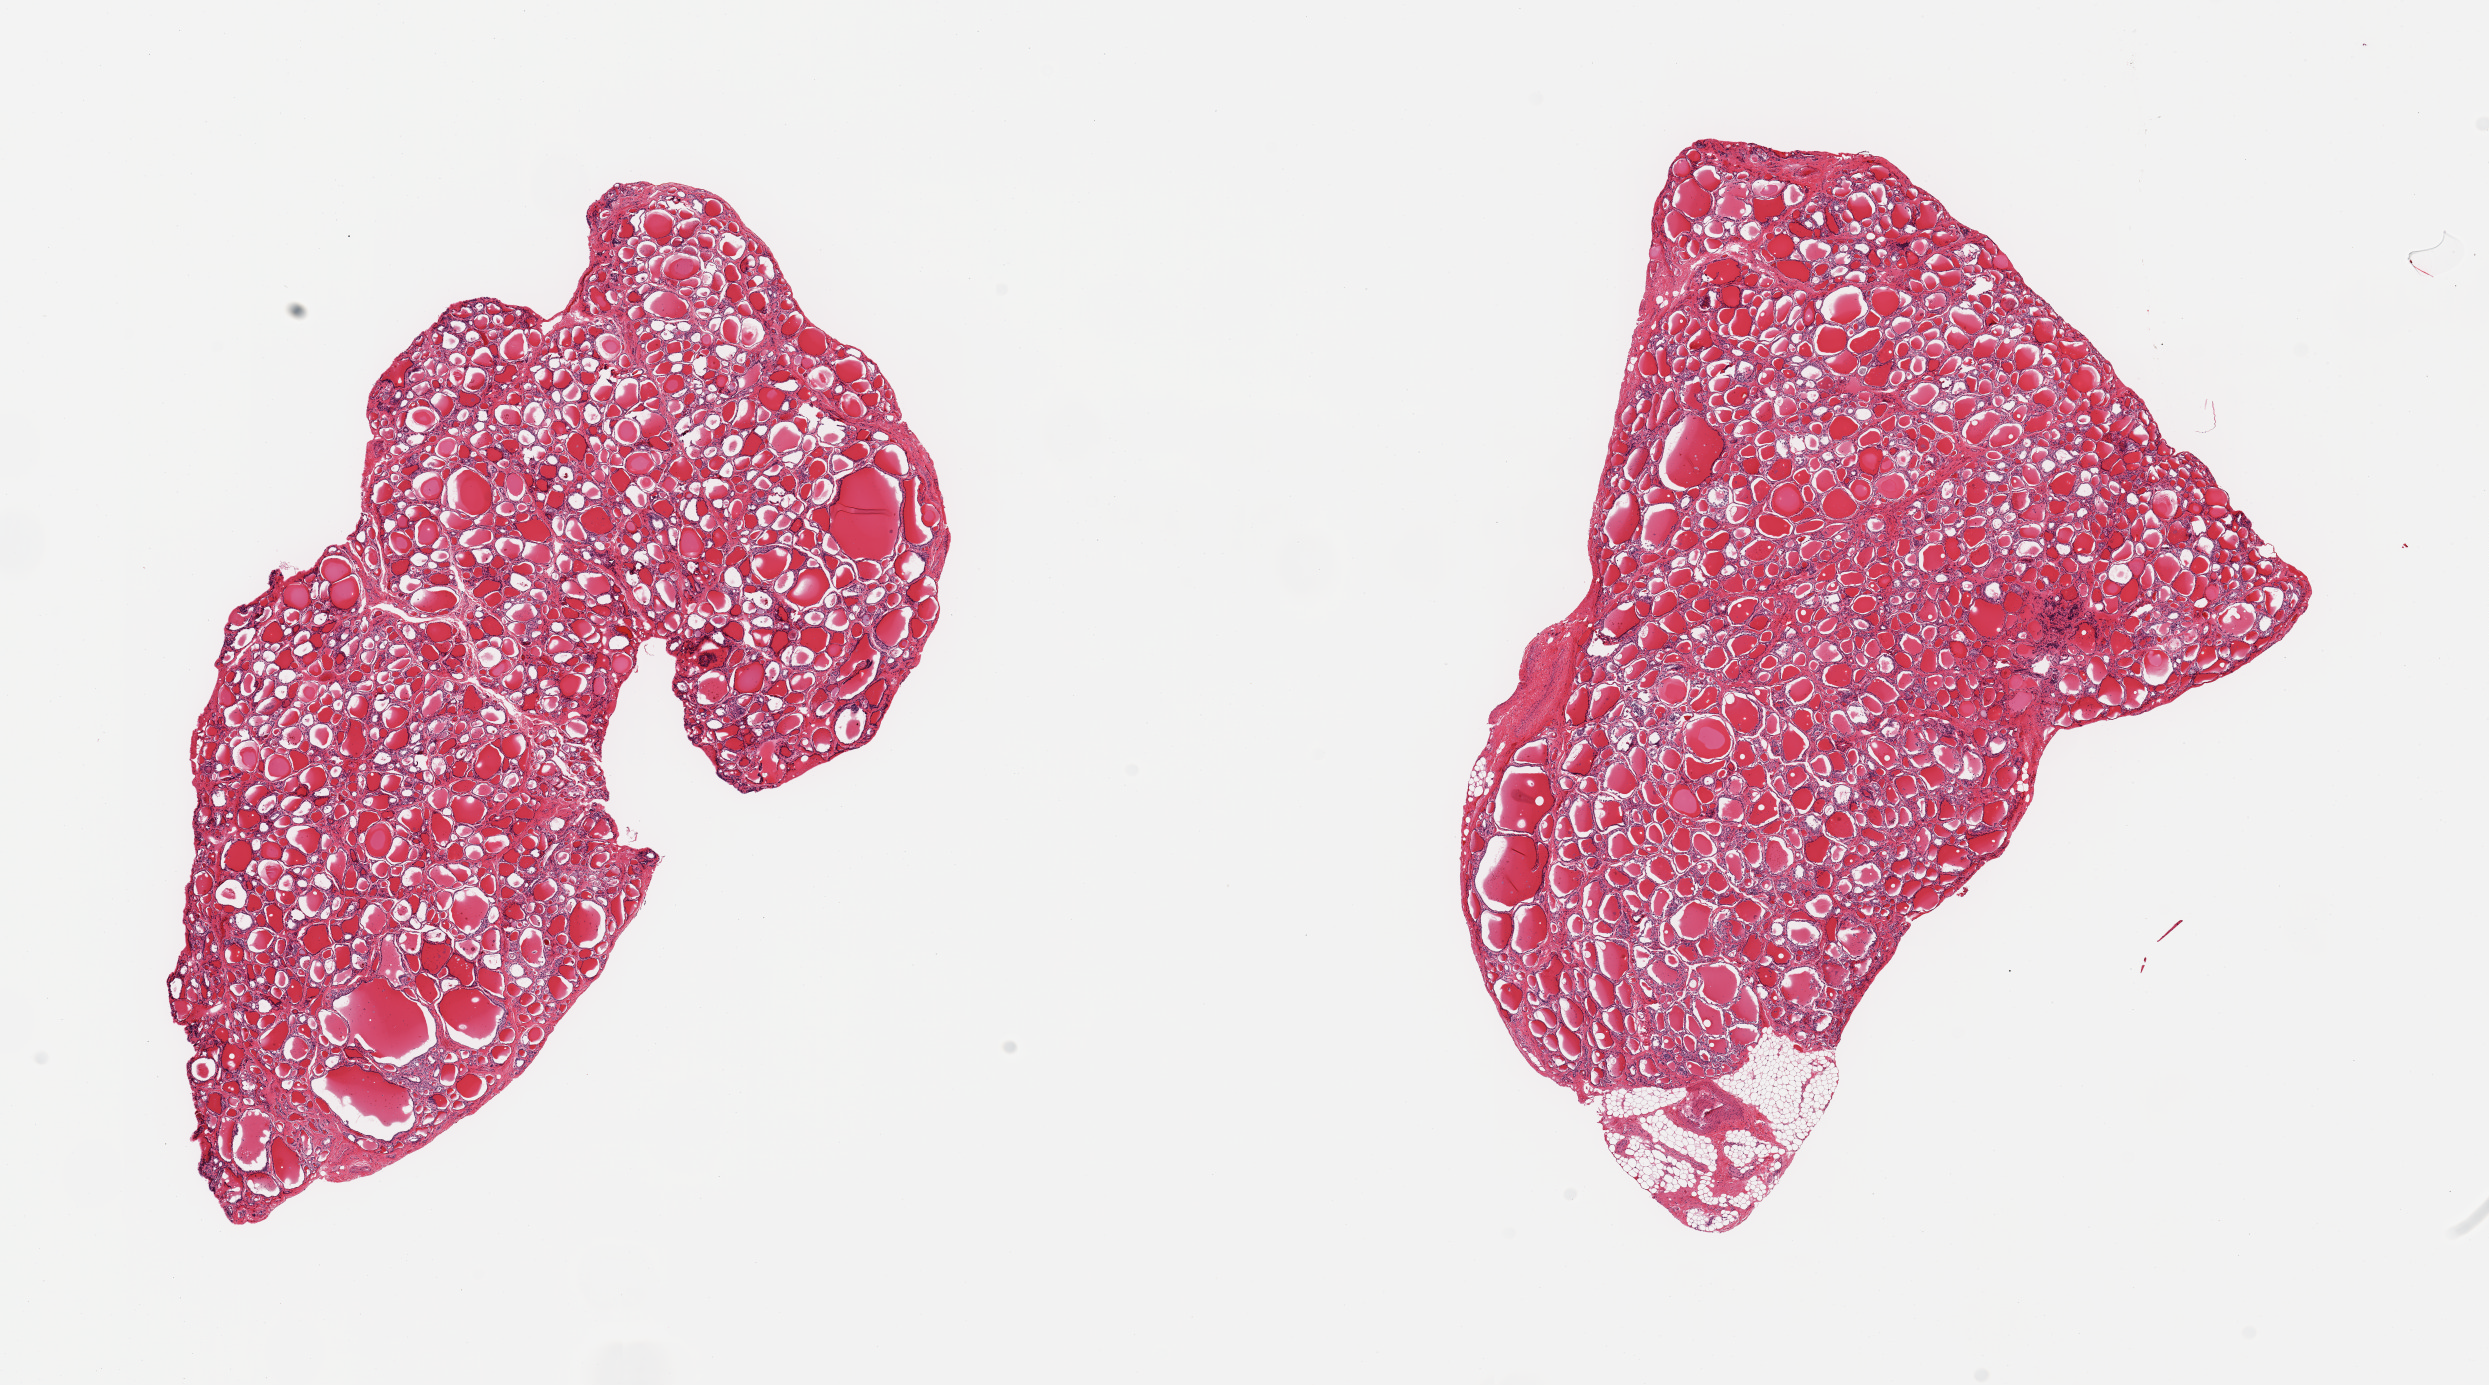
Haematoxylin and eosin whole-slide image, low-resolution overview of the scanned area, about 19.7 x 11.0 mm (acquisition: 20x scan); PAXgene-fixed, paraffin-embedded tissue; sampled site (target tissue): thyroid; donor tissue sample. Donor sex: male.
Review note (as recorded): 2 pieces, no abnormalities; nubbin of adherent fat up to ~1mm.